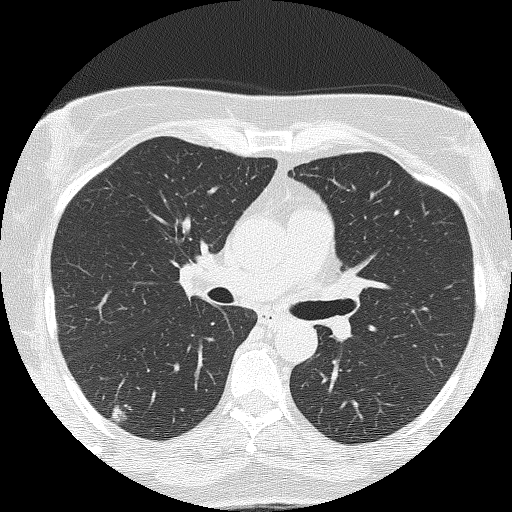
Low-dose screening chest CT, one axial slice; slice 83 of 143 in the series (ordered by position); 120 kVp; lung window (W 1500 / L -600 HU); 2 mm slice thickness; 512 × 512 image matrix, field of view 301 × 301 mm.
Outlined on this slice (outlined manually by an expert reader):
- lesion 1 (tumor, lower lobe of right lung): bounding box [x1, y1, x2, y2] px = [112, 406, 125, 422]